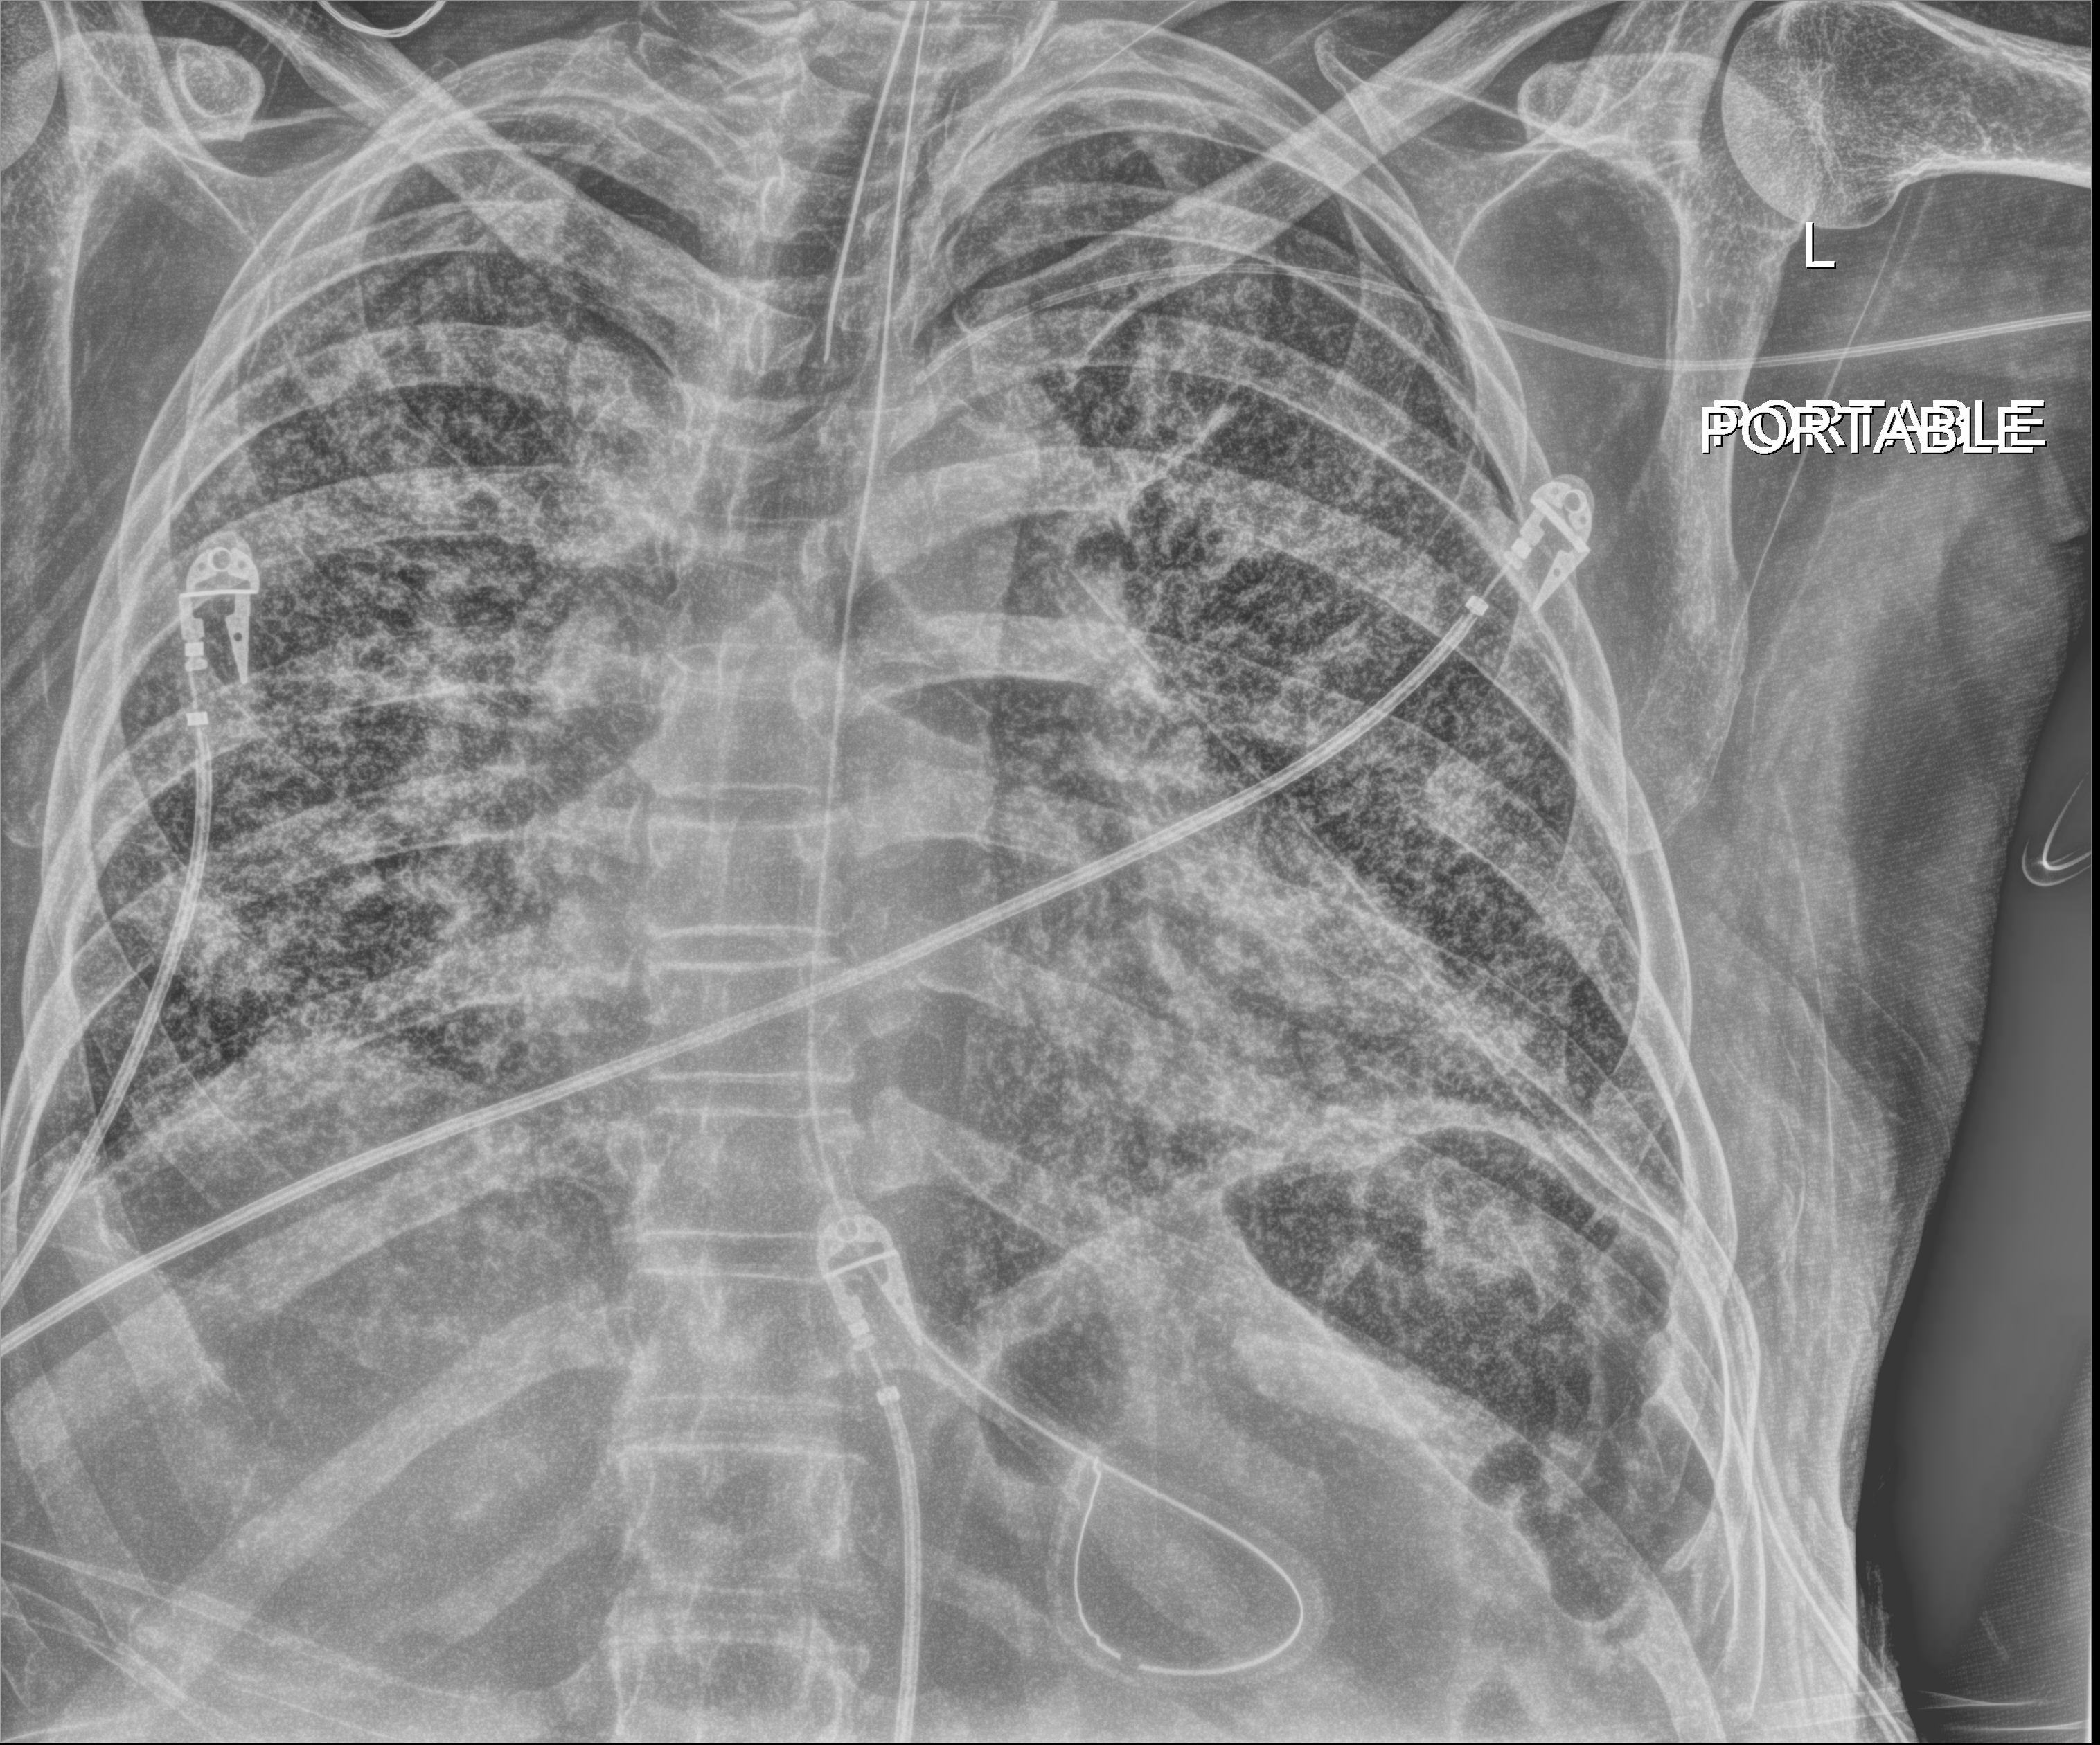
Chest X-ray (portable). Patient hospitalised with COVID-19; male, aged 60–74 years.
From the hospital-stay record, not from the radiograph (when in the stay this image was taken is not recorded): length of hospital stay: 54 days.